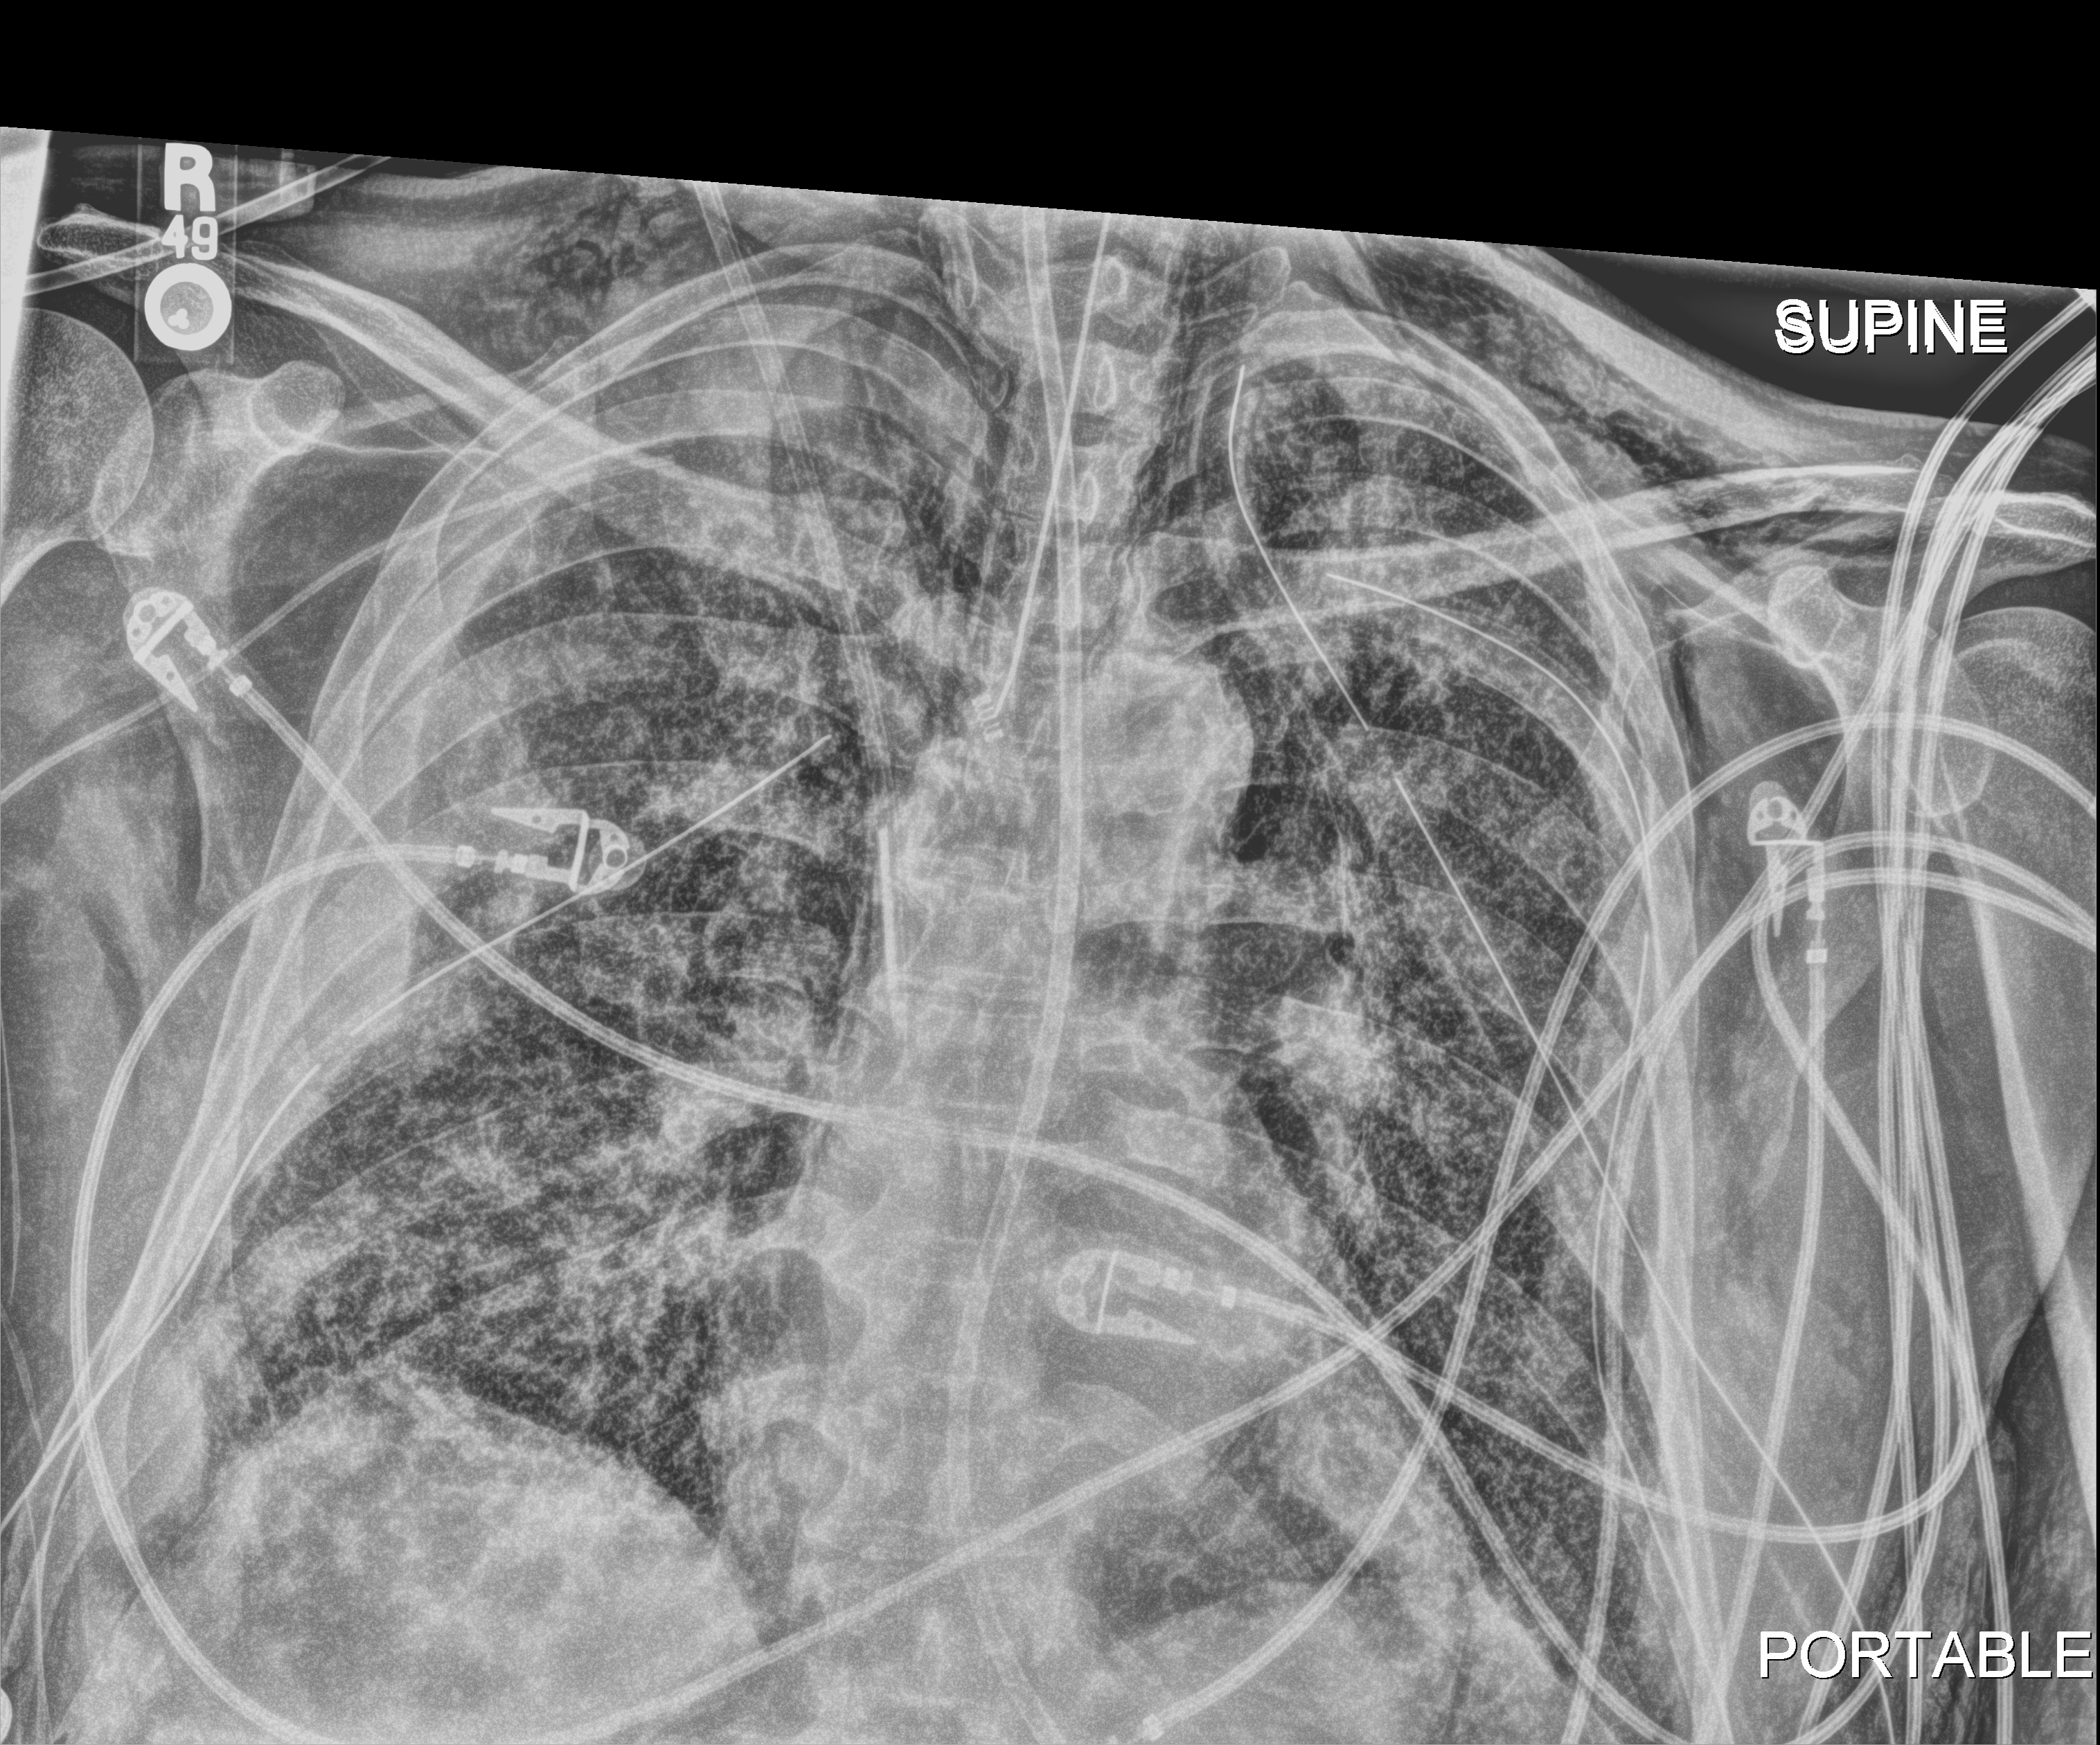
Chest X-ray (portable), anteroposterior (AP) projection. Male patient hospitalised with COVID-19, age 18–59 years.
From the hospital-stay record, not from the radiograph (when in the stay this image was taken is not recorded):
- chronic kidney disease (admission record): no
- admitted to intensive care during this hospital stay: yes